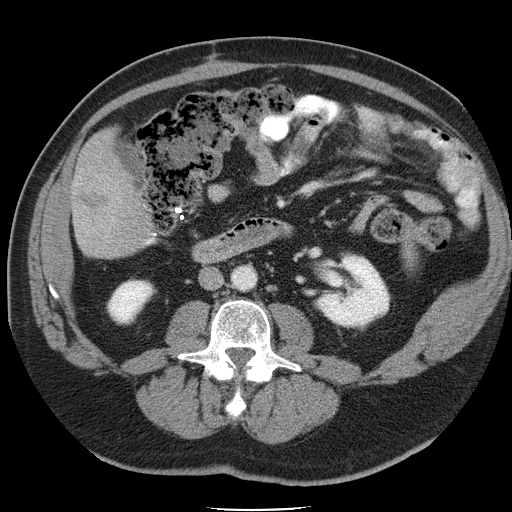
Contrast-enhanced abdominal CT, one axial slice. 120 kVp. Intravenous contrast given. Soft-tissue window (W 400 / L 40 HU). 5 mm slice thickness. 512 × 512 image matrix, field of view 386 × 386 mm. Male patient, age 65 years. Case-level facts recorded for this patient, not image findings: diagnosis: colorectal cancer liver metastases, imaged before liver resection; multiple liver metastases: yes; largest metastasis: 4.9 cm; disease in both lobes: no.
Structures marked on this image (outlined manually by an expert reader):
- liver: bounding box <72,133,144,259> (left, top, right, bottom; pixels)
- planned liver remnant (the part of the liver to remain after resection): <103,135,108,140>
- liver metastasis: <78,182,108,220>